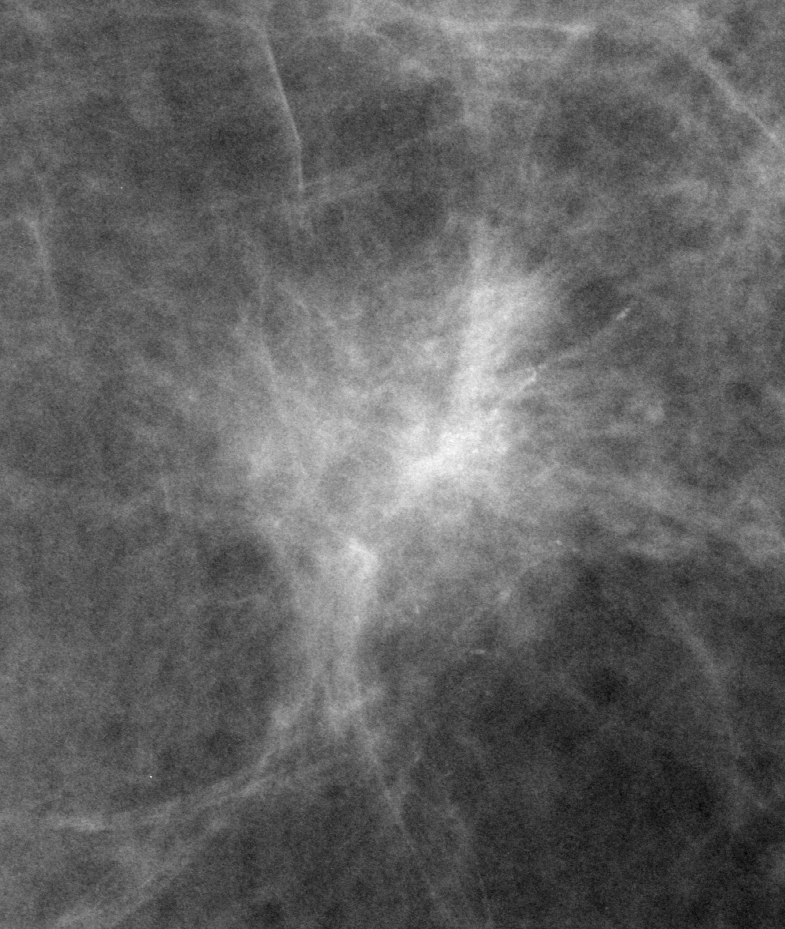
Region of interest cut from a scanned film mammogram (one marked finding), left breast, CC view, BI-RADS breast density category 1 (scale 1–4).
Calcifications, morphology amorphous, distribution clustered; BI-RADS assessment category 5; pathology (as recorded): malignant.